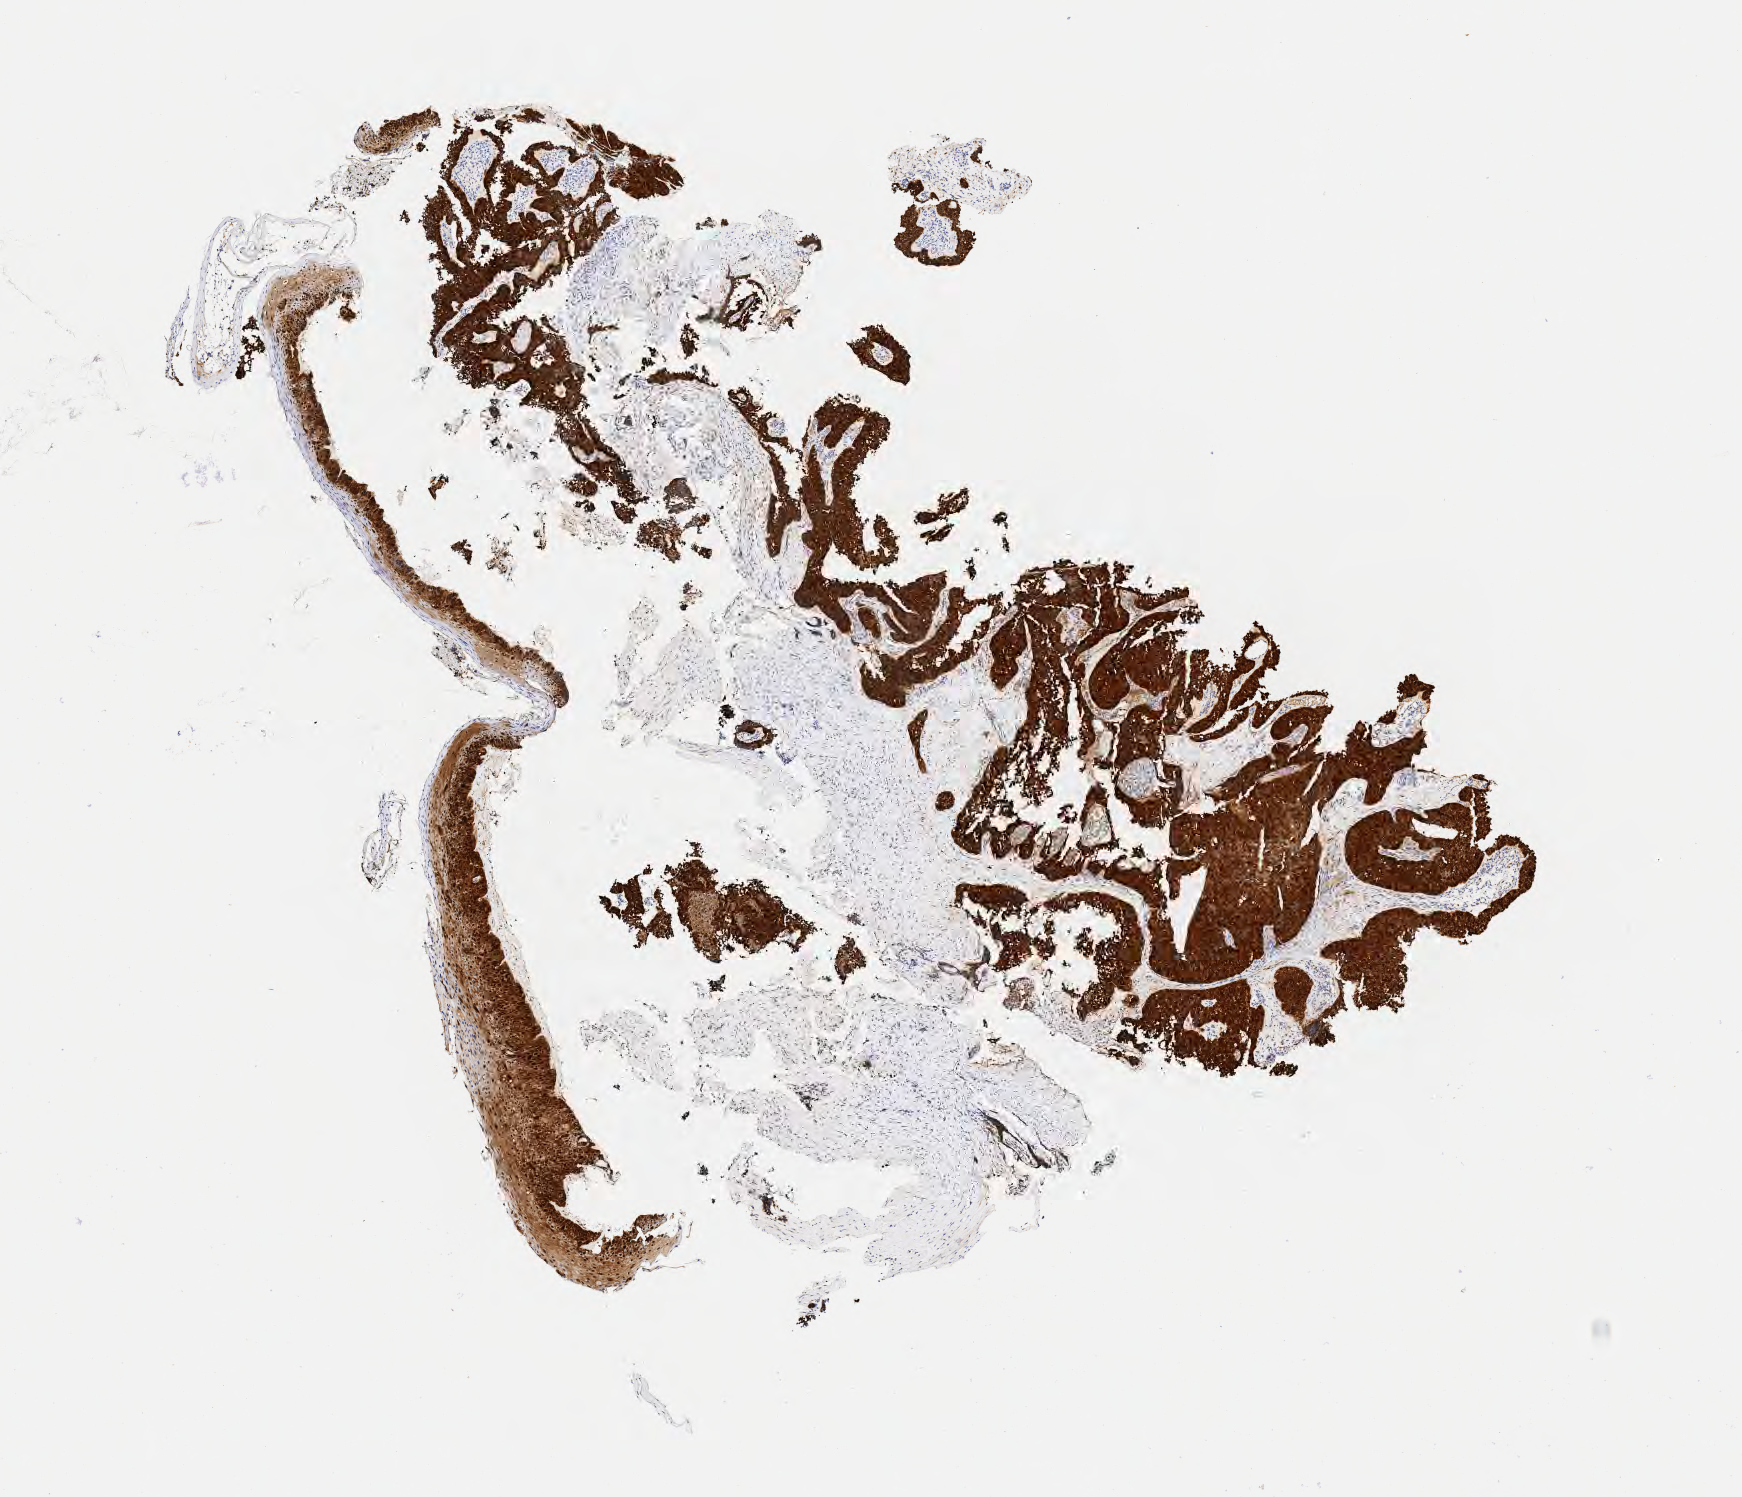
Whole-slide image, immunohistochemical stain for p16 (p16INK4a), shown as a low-resolution overview of the whole scanned area (about 7.0 x 6.1 mm), tumor tissue, site: cervix. Patient: female, age 53 years.
* diagnosis: Squamous cell carcinoma, large cell, nonkeratinizing, NOS